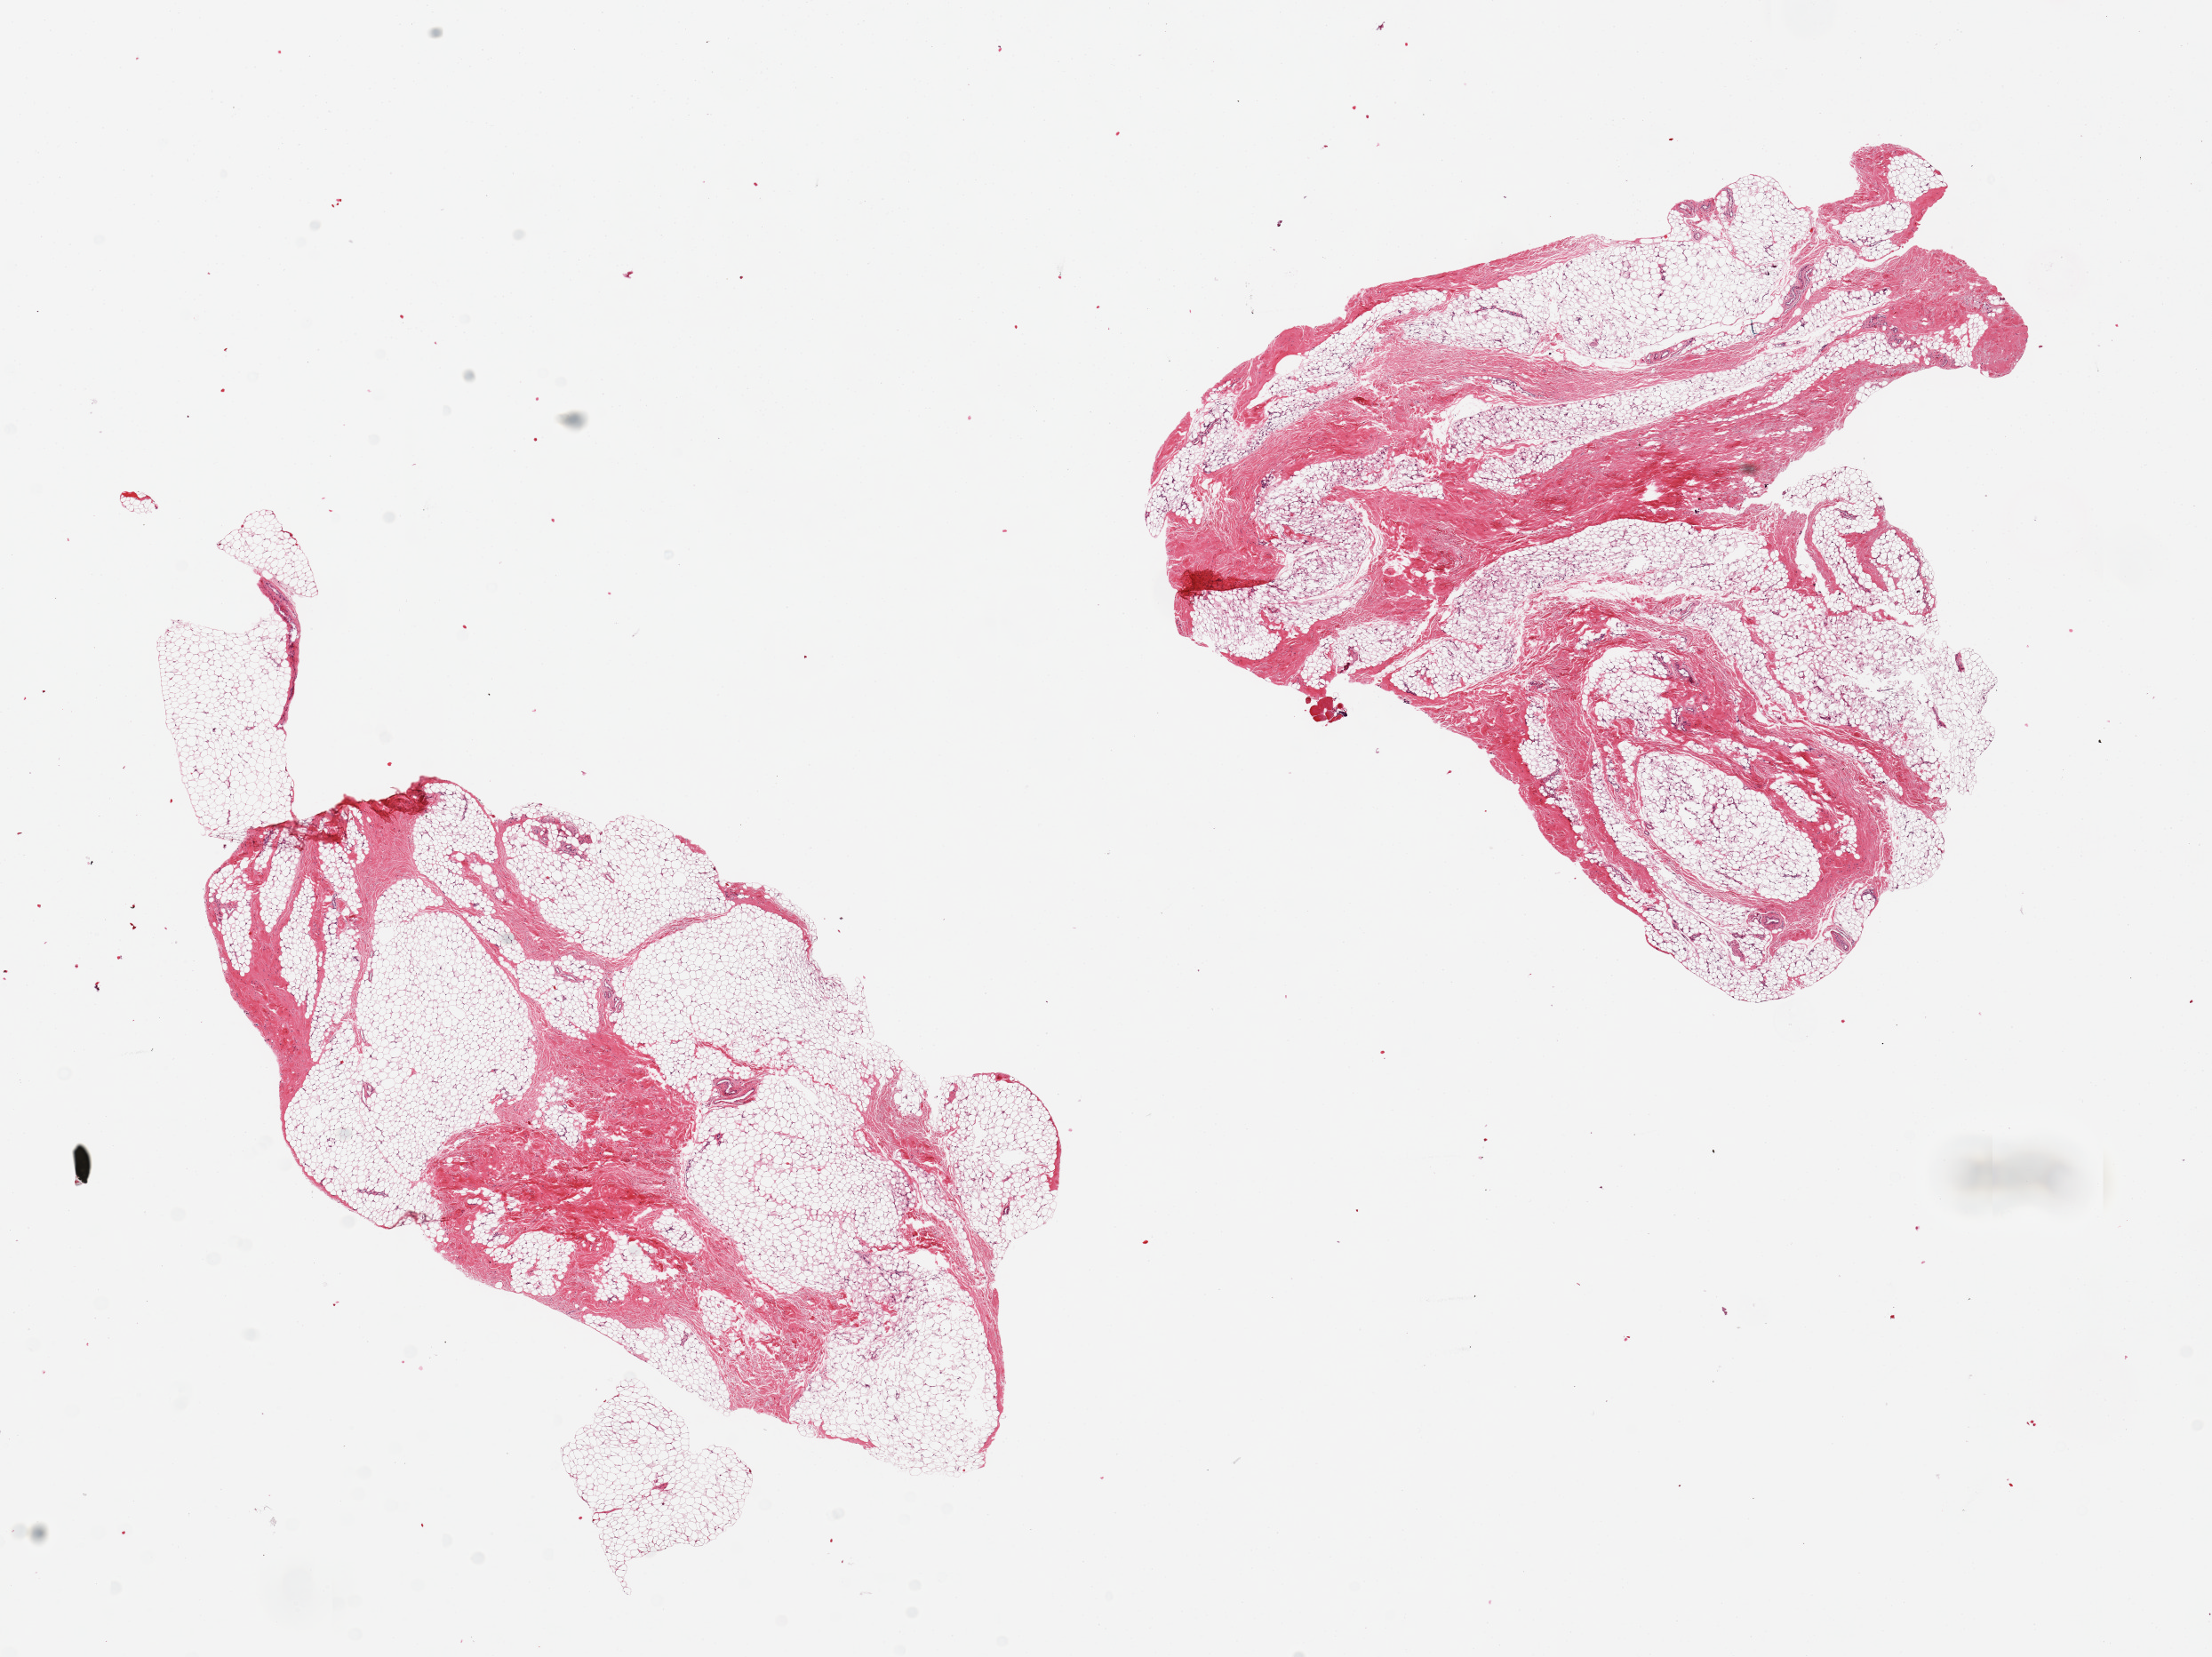
Hematoxylin and eosin (H&E) whole-slide image, low-resolution overview of the scanned area, about 19.7 x 14.8 mm (acquisition: 20x scan); PAXgene-fixed paraffin-embedded (PFPE) section; section of breast (target tissue); tissue donor sample. Donor: male.
Review note (as recorded): 2 pieces, both ~50% fibrous tissue; rest adipose; No ductal elements.